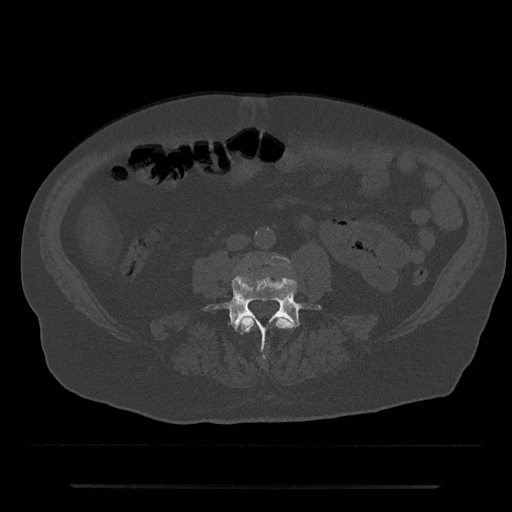
CT including the spine, one axial slice. Position 366 of 797 along the scan axis. Reconstruction kernel Br40s/3. Bone window (W 1800 / L 400 HU). 512 × 512 image matrix, field of view 434 × 434 mm. Patient: male, 80 years. From the clinical record (not read from this slice): primary cancer: prostate; vertebrae with lytic lesions (as recorded): L1, T11.
Outlined on this slice (semi-automatic segmentation, software-assisted and operator-edited):
- L3 vertebra: box from (x=238, y=316) to (x=293, y=333) px
- L4 vertebra: (x=204, y=274)–(x=322, y=359)